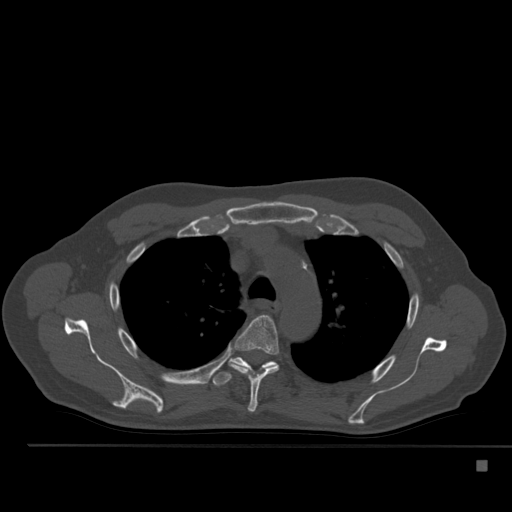
CT including the spine, one axial slice. Slice 377 of 517 in the series (ordered by position). 120 kVp. Bone window (W 1800 / L 400 HU). 1.5 mm slice thickness. 512 × 512 image matrix. Patient: male, 70 years. Case-level facts recorded for this patient, not image findings: primary cancer: renal.
Outlined on this slice (semi-automatically segmented with operator editing):
- T4 vertebra: bounding box <231,315,280,412> (left, top, right, bottom; pixels)
- T5 vertebra: <212,357,277,387>